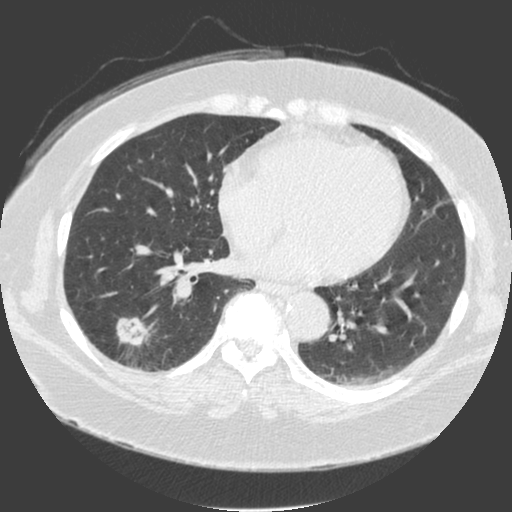
Low-dose screening chest CT, one axial slice. Slice 75 of 175 in the series (ordered by position). 120 kVp. Lung window (W 1500 / L -600 HU). 2 mm slice thickness. 512 × 512 image matrix, field of view 370 × 370 mm.
Annotated regions visible in this slice (outlined manually by an expert reader):
- lesion 1 (tumor, lower lobe of right lung): box from (x=117, y=318) to (x=151, y=345) px